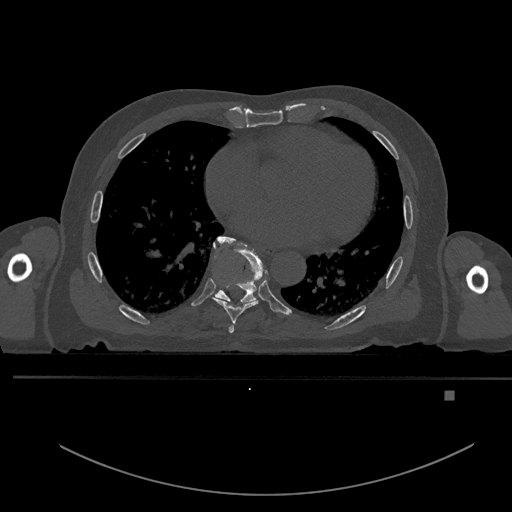
CT including the spine, one axial slice; slice 232 of 969 in the series (ordered by position); bone window (W 1800 / L 400 HU); 0.5 mm slice thickness; 512 × 512 image matrix, field of view 456 × 456 mm. Patient: male, 82 years. Case-level facts recorded for this patient, not image findings: primary cancer: prostate; vertebrae with lytic lesions (as recorded): T11, T9, T8, T2.
Annotated regions visible in this slice (semi-automatically segmented with operator editing):
- T6 vertebra: box from (x=228, y=324) to (x=234, y=333) px
- T7 vertebra: (x=213, y=235)–(x=268, y=324)
- T8 vertebra: (x=213, y=239)–(x=263, y=308)